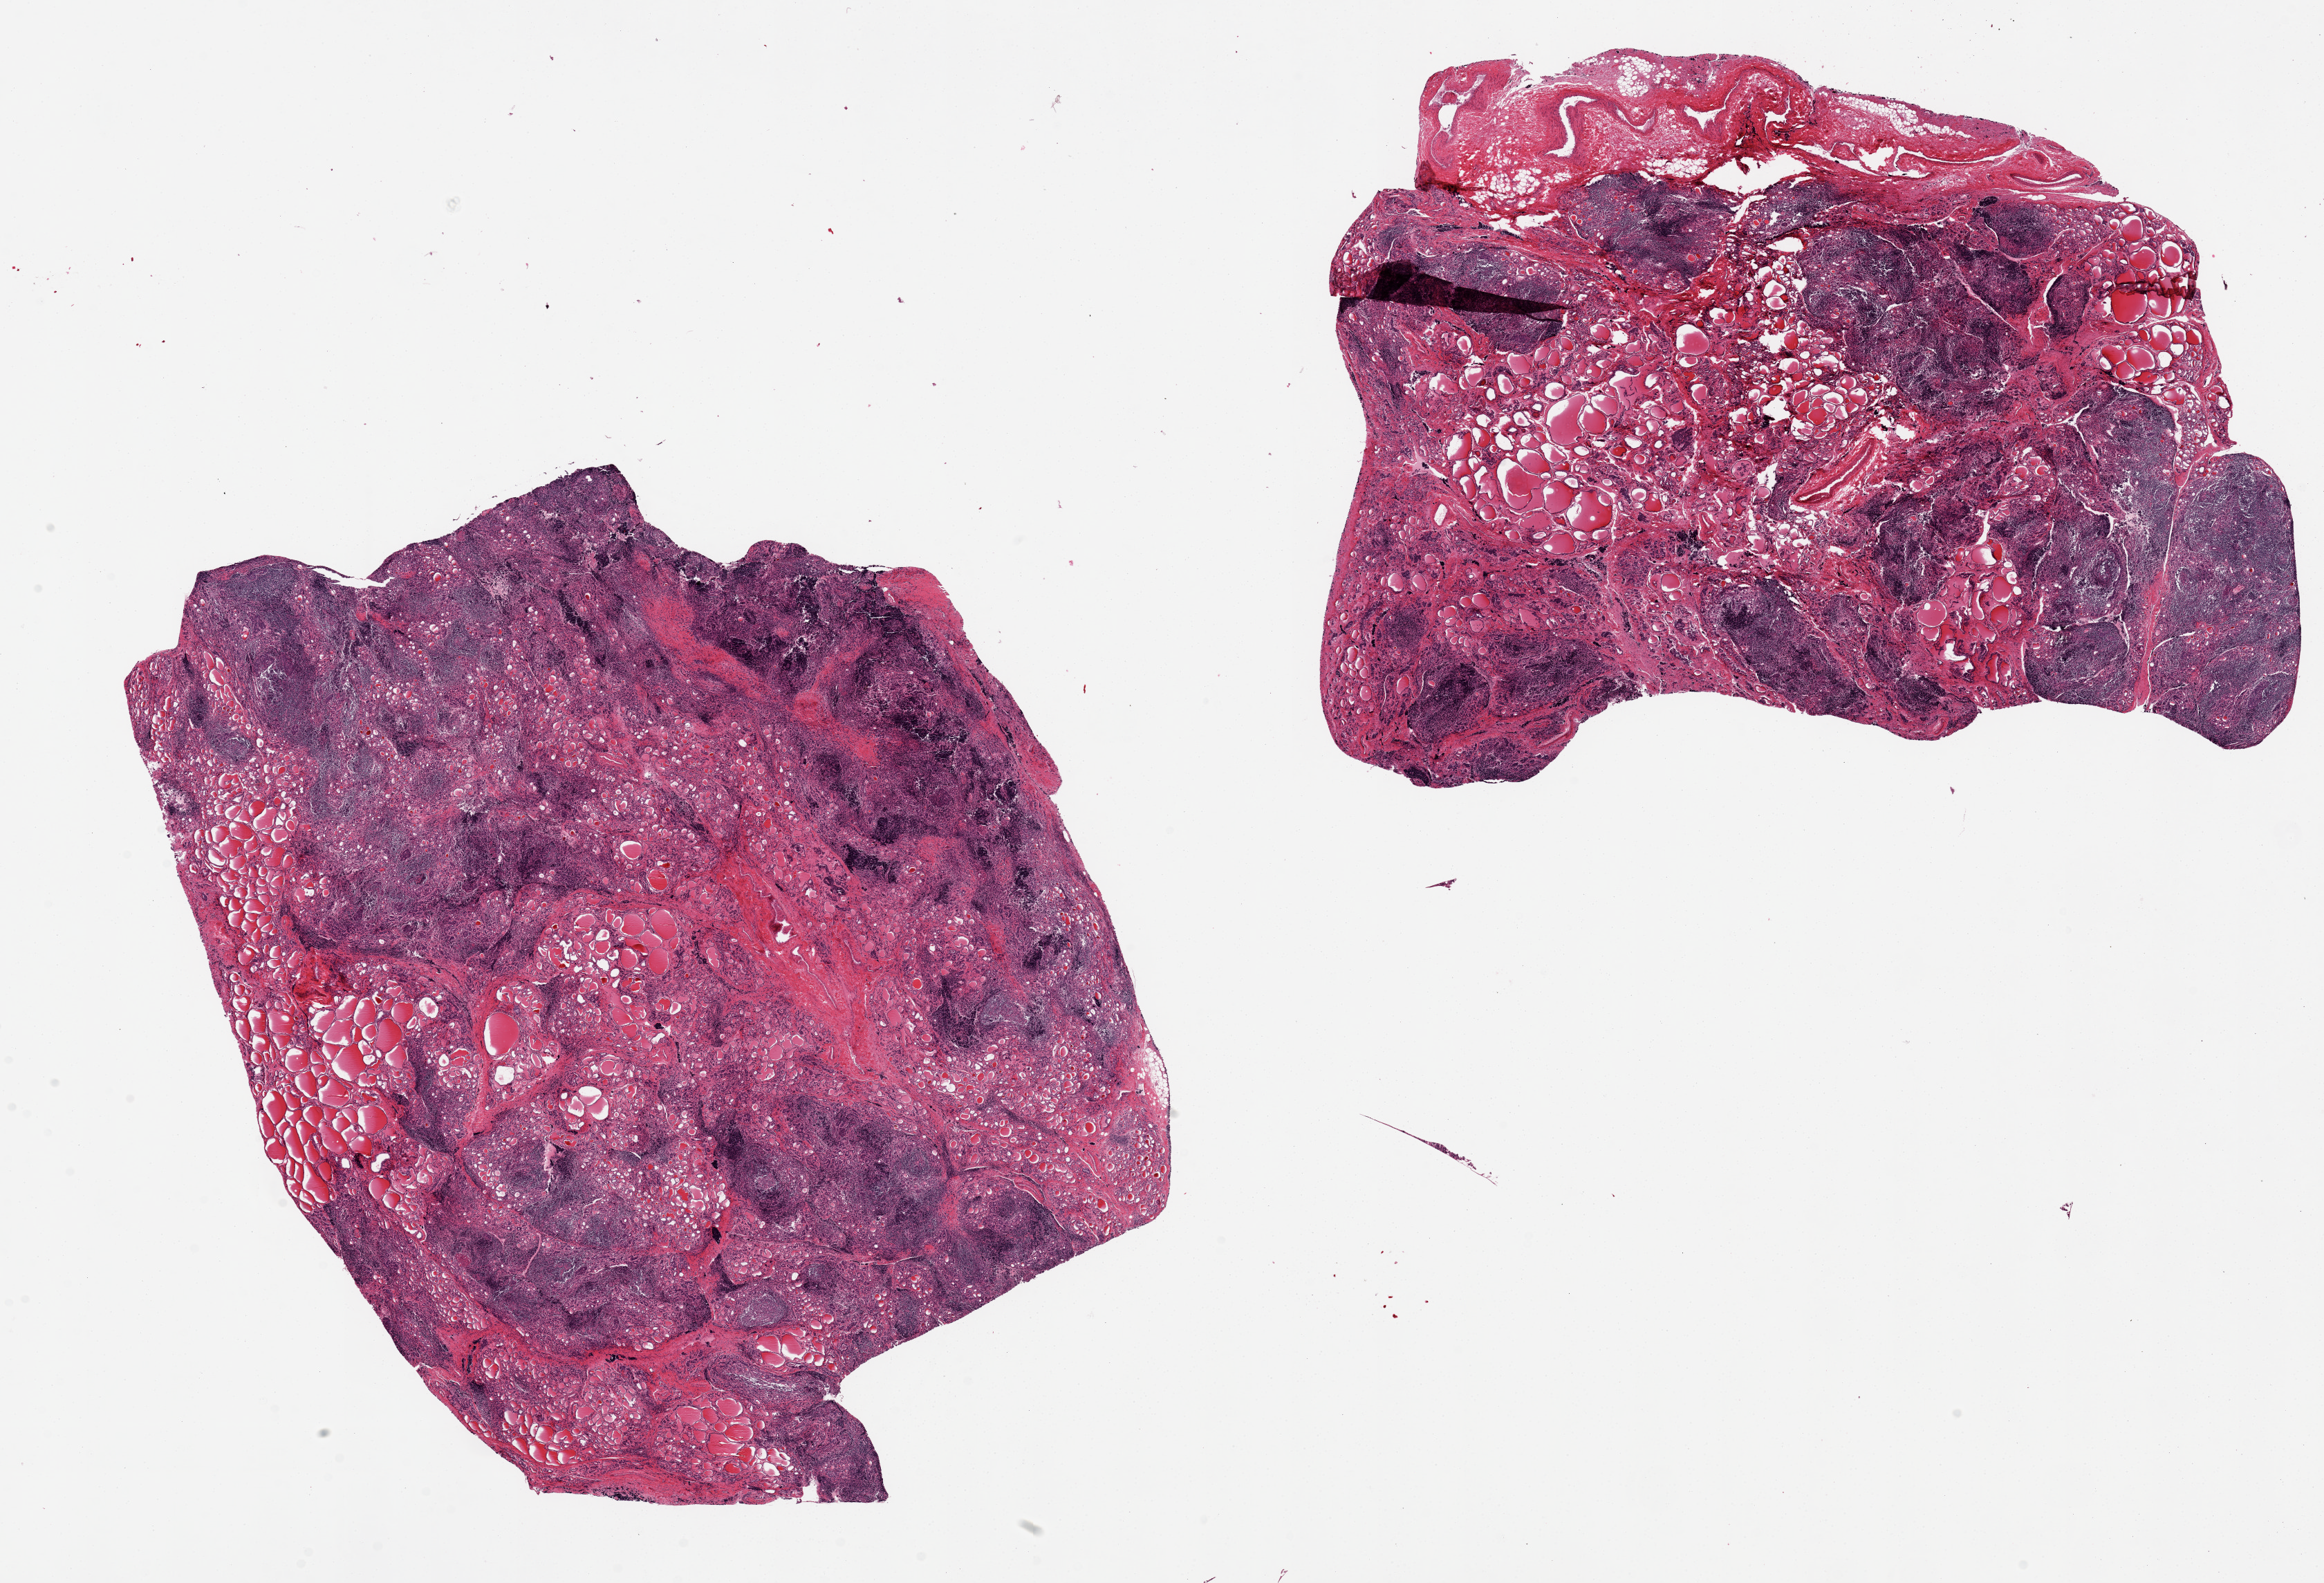
Digitized hematoxylin and eosin (H&E)-stained section, brightfield — whole scanned area (about 26.6 x 18.1 mm, from a 20x scan) shown as a low-resolution overview, PAXgene-fixed paraffin-embedded (PFPE) section, sampled site (target tissue): thyroid, tissue donor sample. Male donor.
Reviewer comment on this tissue sample: 2 pieces; Hashimoto thyroiditis with marked lymphocytic infiltrate and atrophy.